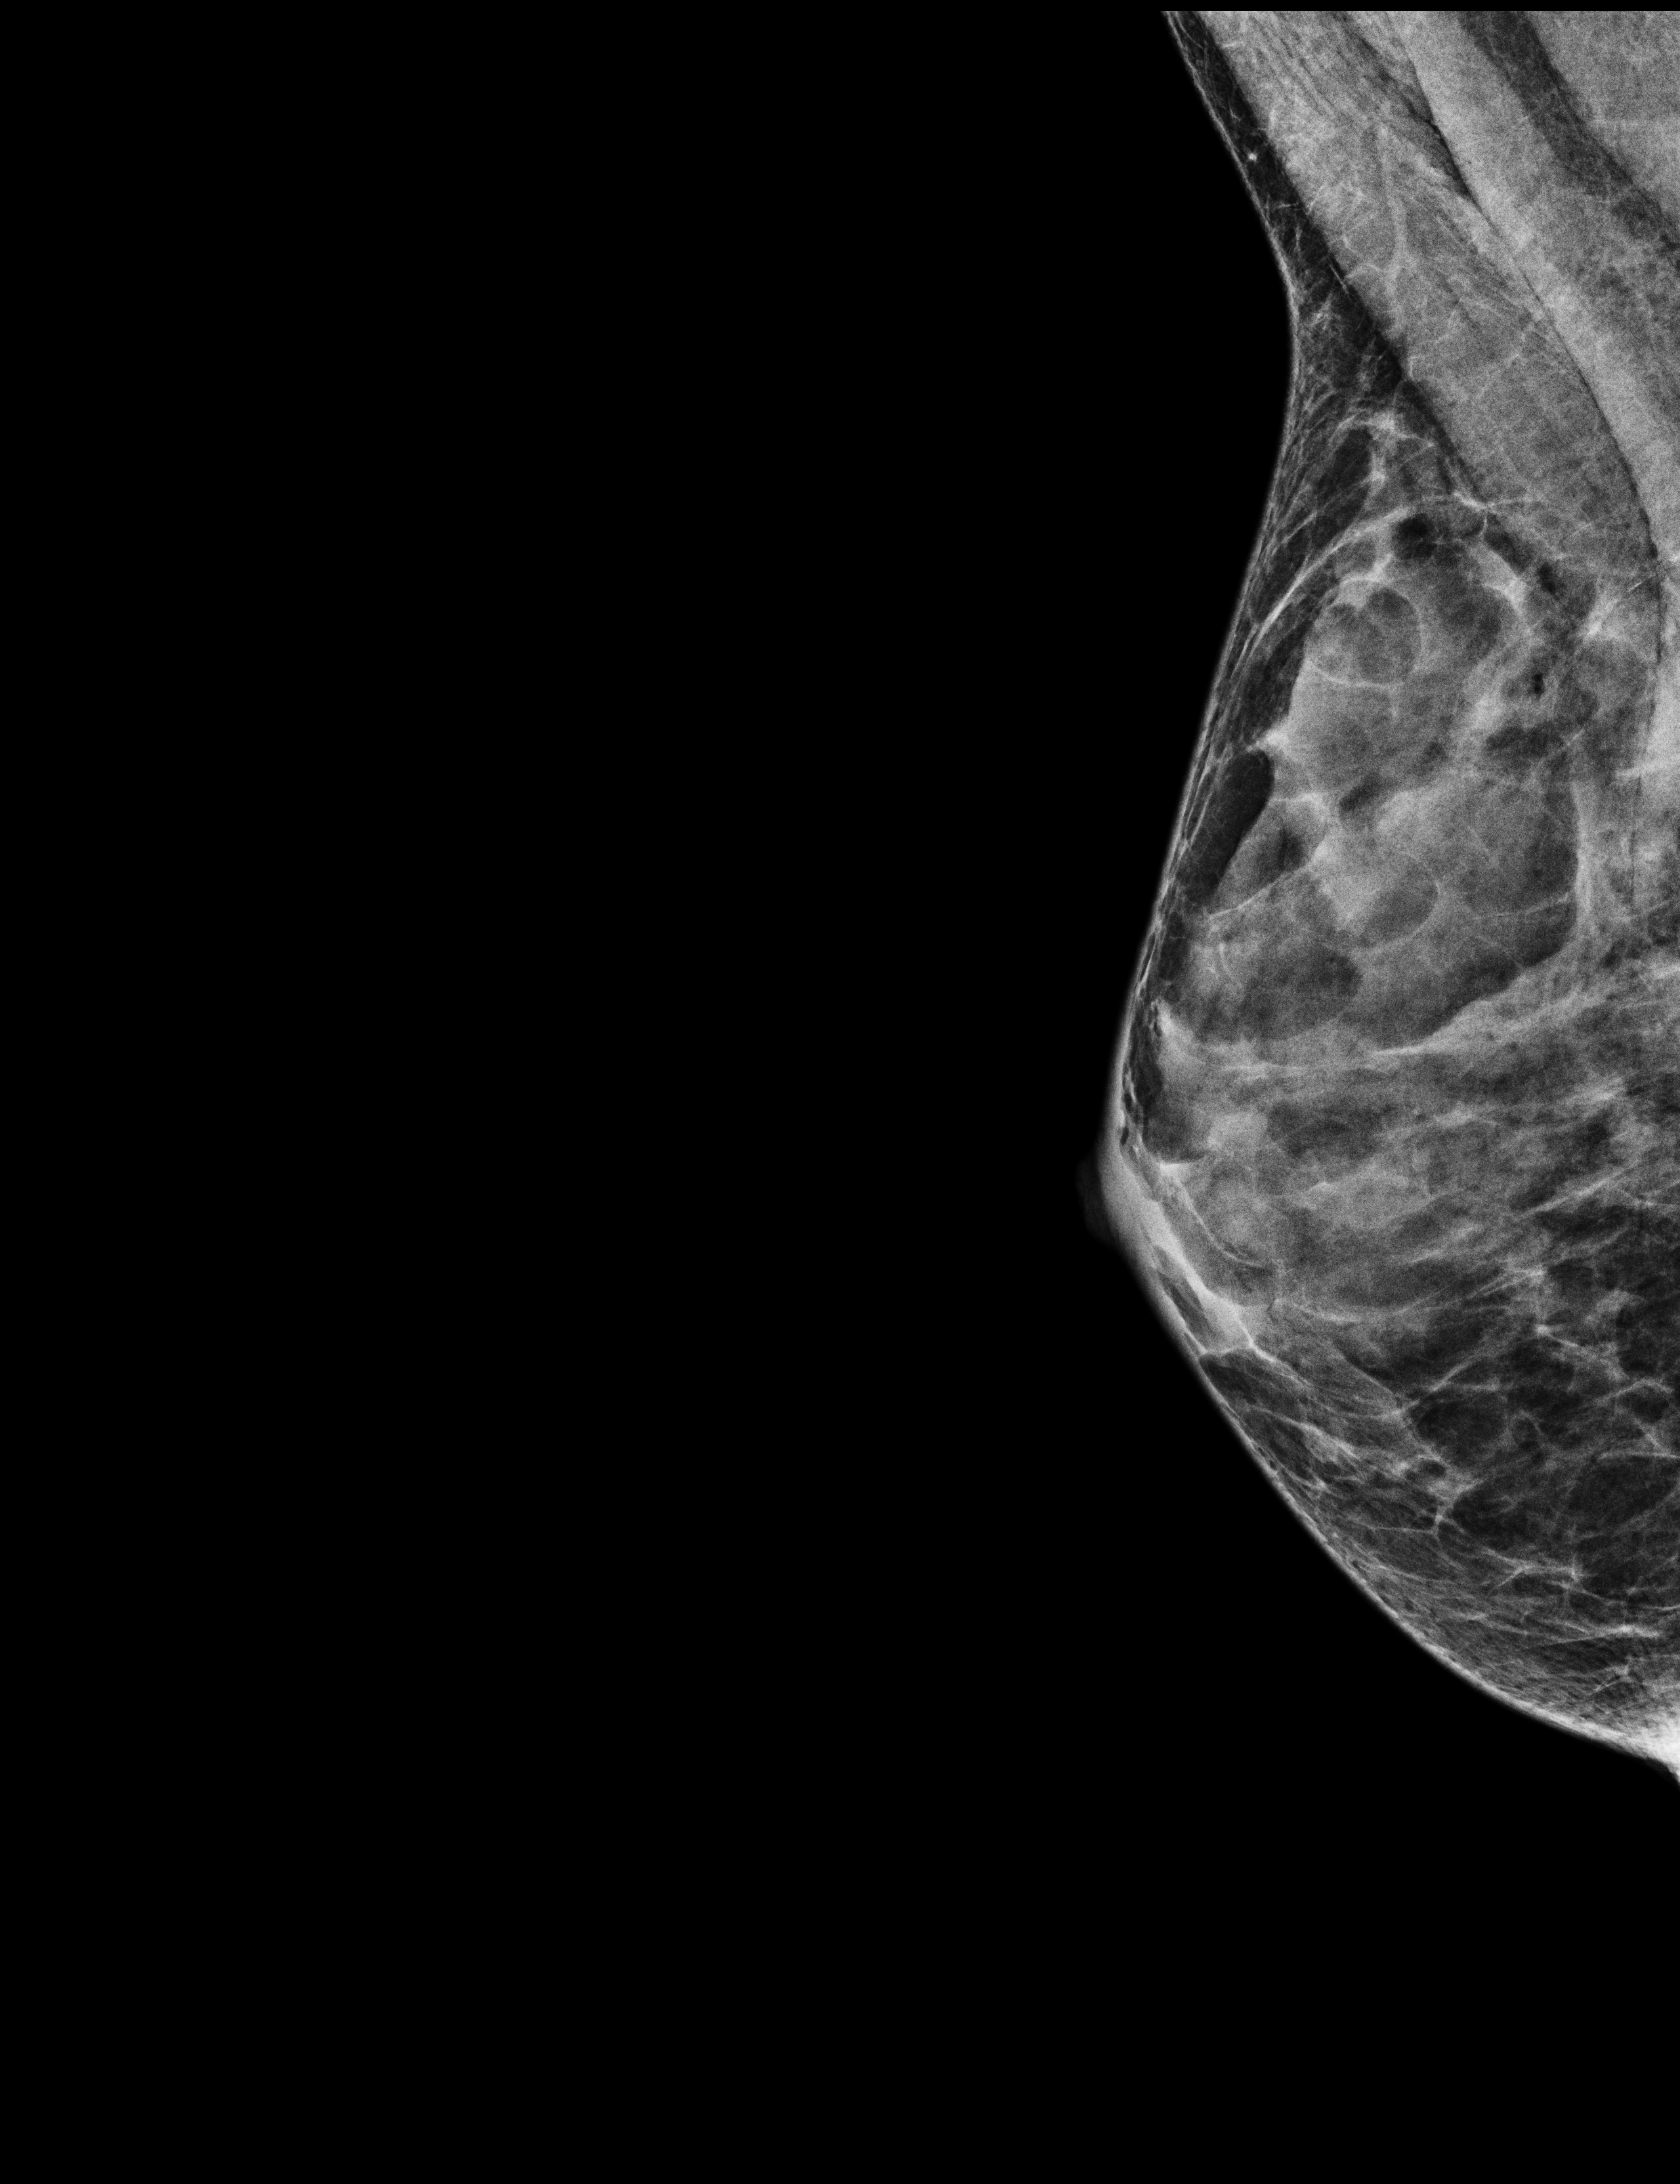
Digital mammogram (FFDM); right breast; mediolateral oblique (MLO) view; annual screening mammography examination; compressed breast thickness 21 mm. Patient aged 68 years (female).
BI-RADS breast density category at the screening exam (both breasts, scale 1–4): 4. Final BI-RADS assessment for this screening round (tomosynthesis exam, both breasts): category 1. Recall: no recall after this screen.